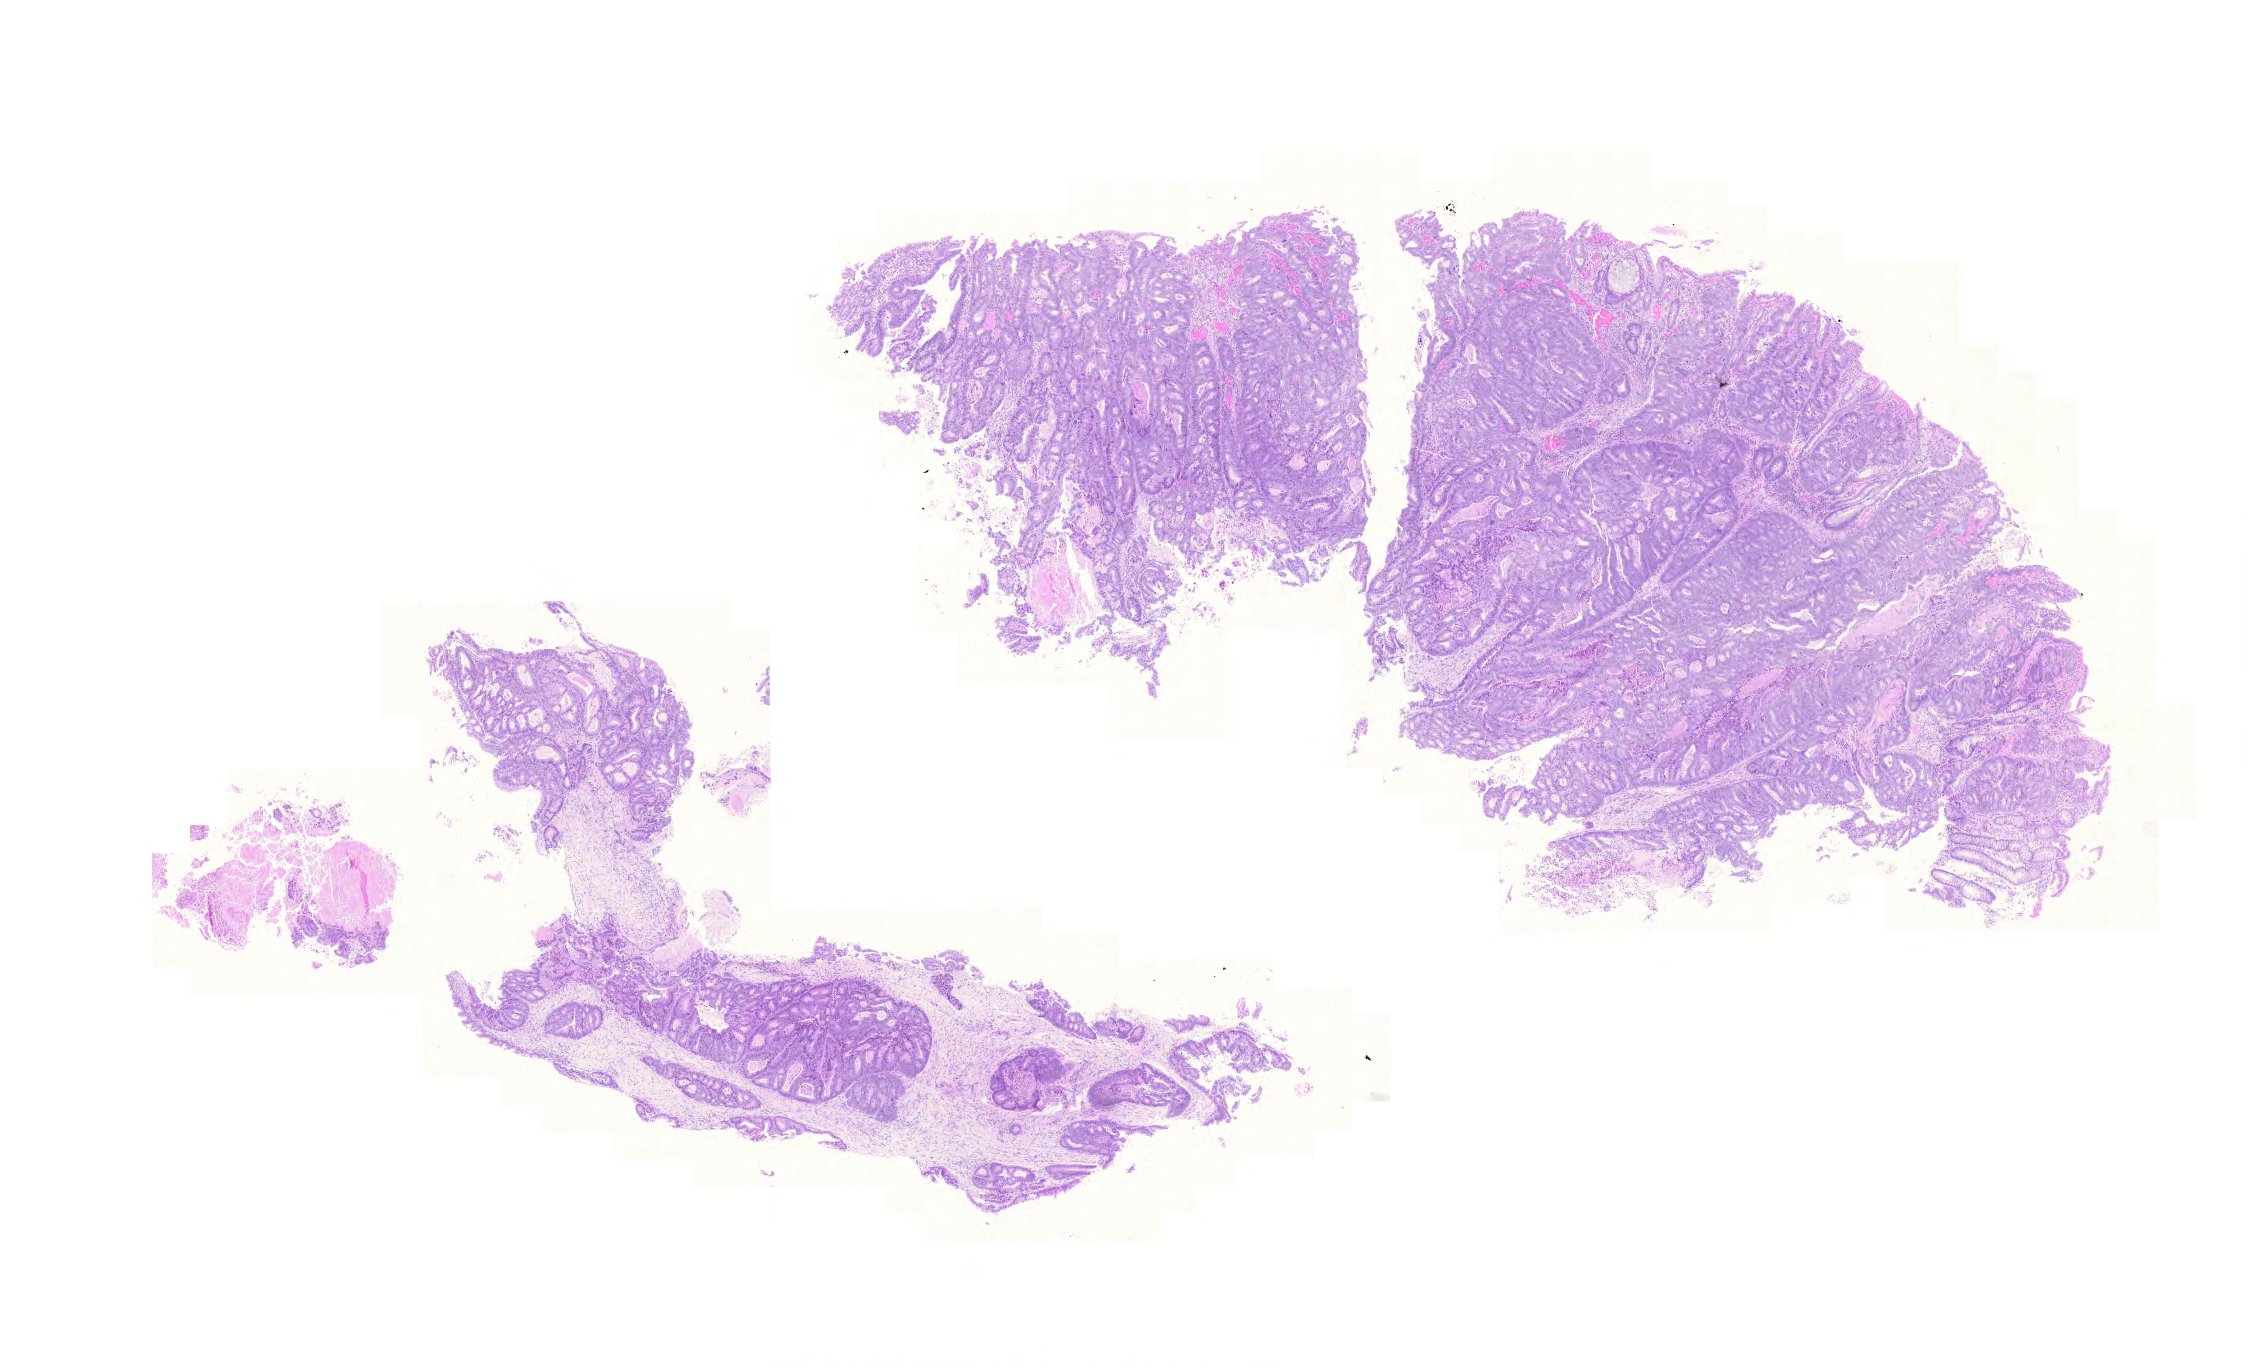
Digitized Hematoxylin and eosin (H&E) stained tissue section (whole slide), a low-resolution overview of the entire scanned area, about 16.7 x 10.2 mm (from a 20x scan), formalin-fixed paraffin-embedded (FFPE) diagnostic section, primary tumour sample from the rectum. Patient sex: female.
- lymph nodes positive (case pathology): 0 of 18 examined
- diagnosis: Adenocarcinoma, NOS
- AJCC pathologic stage: II (5th edition)